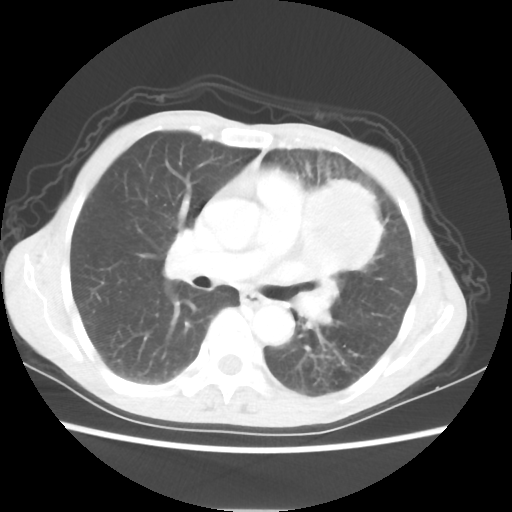
Chest CT, one axial slice. Position 34 of 56 along the scan axis. Lung window (W 1500 / L -600 HU). 5 mm slice thickness. 512 × 512 image matrix, field of view 331 × 331 mm. Female patient, age 60 years. Case-level facts recorded for this patient, not image findings: clinical TNM (as recorded): T4 N1 M0.
Outlined on this slice (rectangle marked by the reading radiologist):
- lung tumour (recorded histology: adenocarcinoma): bounding box <296,174,385,279> (left, top, right, bottom; pixels)